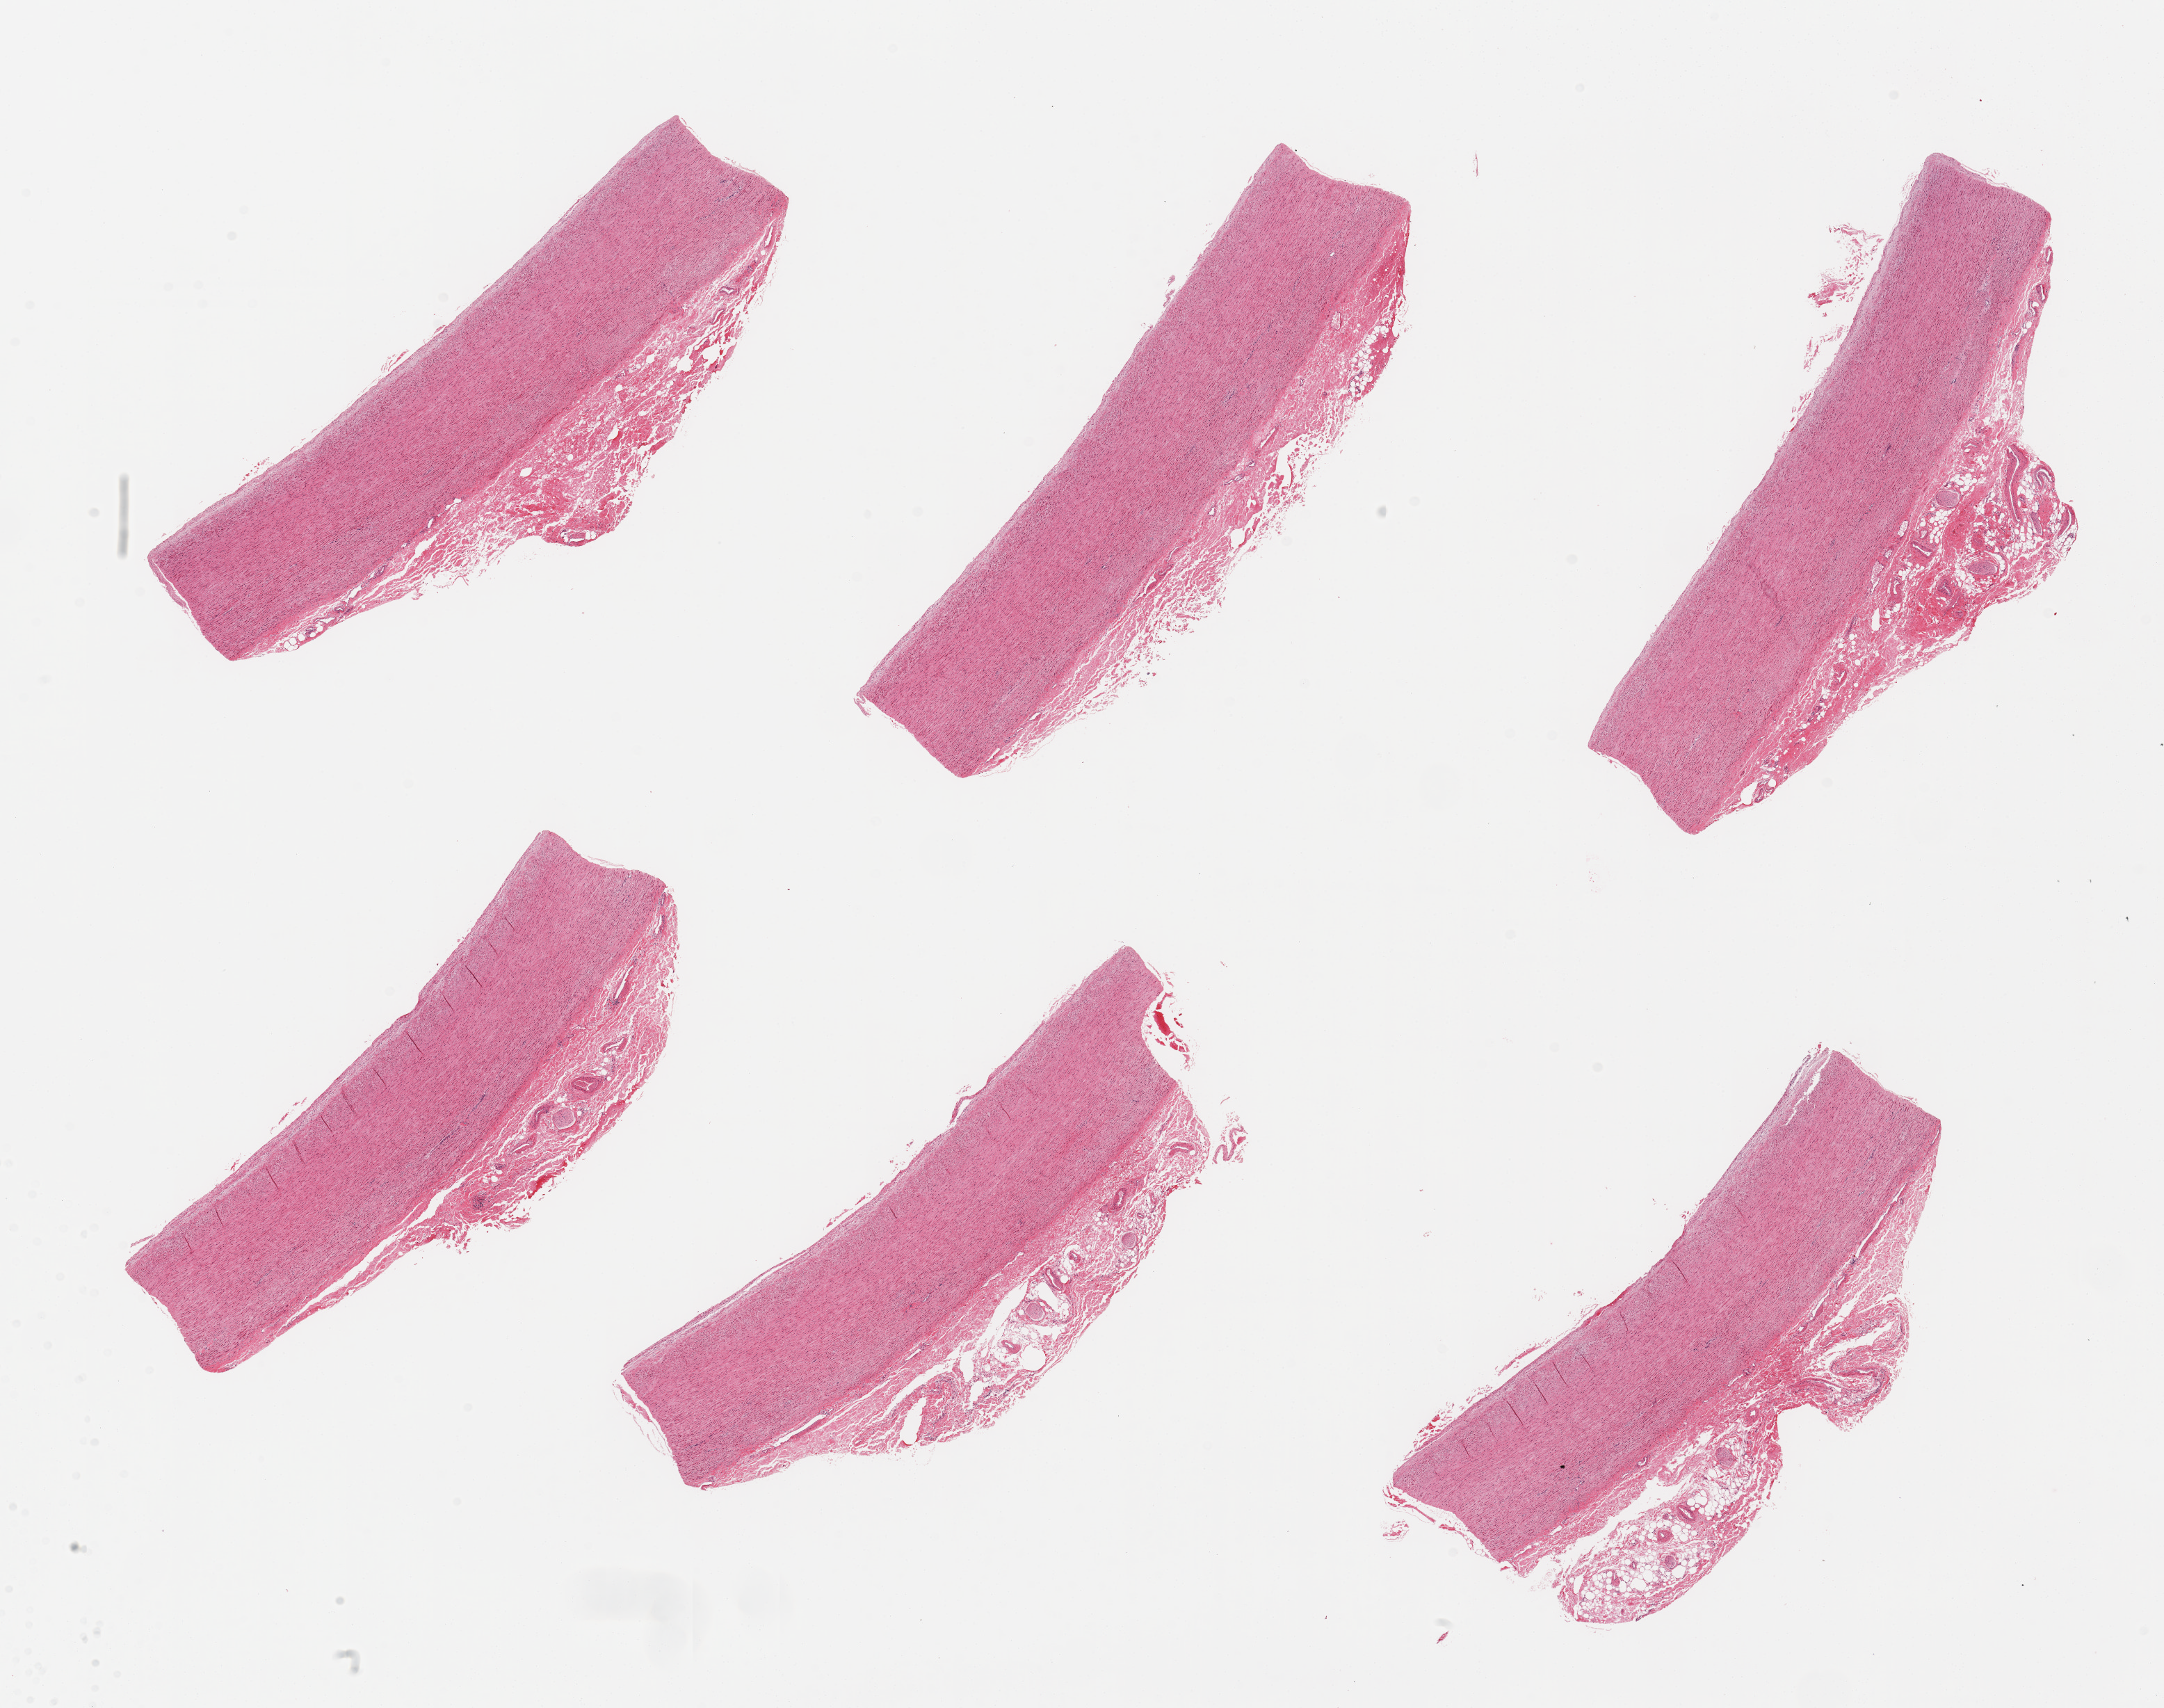
Hematoxylin and eosin (H&E) whole-slide image — whole scanned area (about 24.6 x 19.4 mm) shown as a low-resolution overview. PAXgene-fixed, paraffin-embedded tissue. Section of aorta (target tissue). Donor tissue sample. Male donor.
Review note (as recorded): 6 pieces; no plaque; all have up to 1.6mm adventitial fibrofatty stroma.